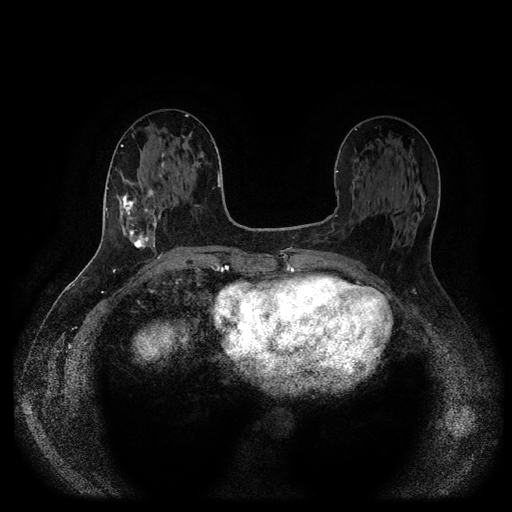
Breast MRI (dynamic contrast-enhanced, multi-phase), one axial slice. Slice 45 of 116 in the series (ordered by position). Dynamic contrast-enhanced series, time point 2 of 5 at this slice position (early post-contrast). 1.5 T. TE 2.6 ms, TR 5.3 ms. 2 mm slice thickness. 512 × 512 image matrix, field of view 360 × 360 mm. Patient: female, 58 years.
Structures marked on this image (semi-automatically segmented with operator editing):
- breast lesion (labelled 'tumour' in the annotation; benign lesions carry a separate 'benign' label): box from (x=119, y=187) to (x=162, y=252) px